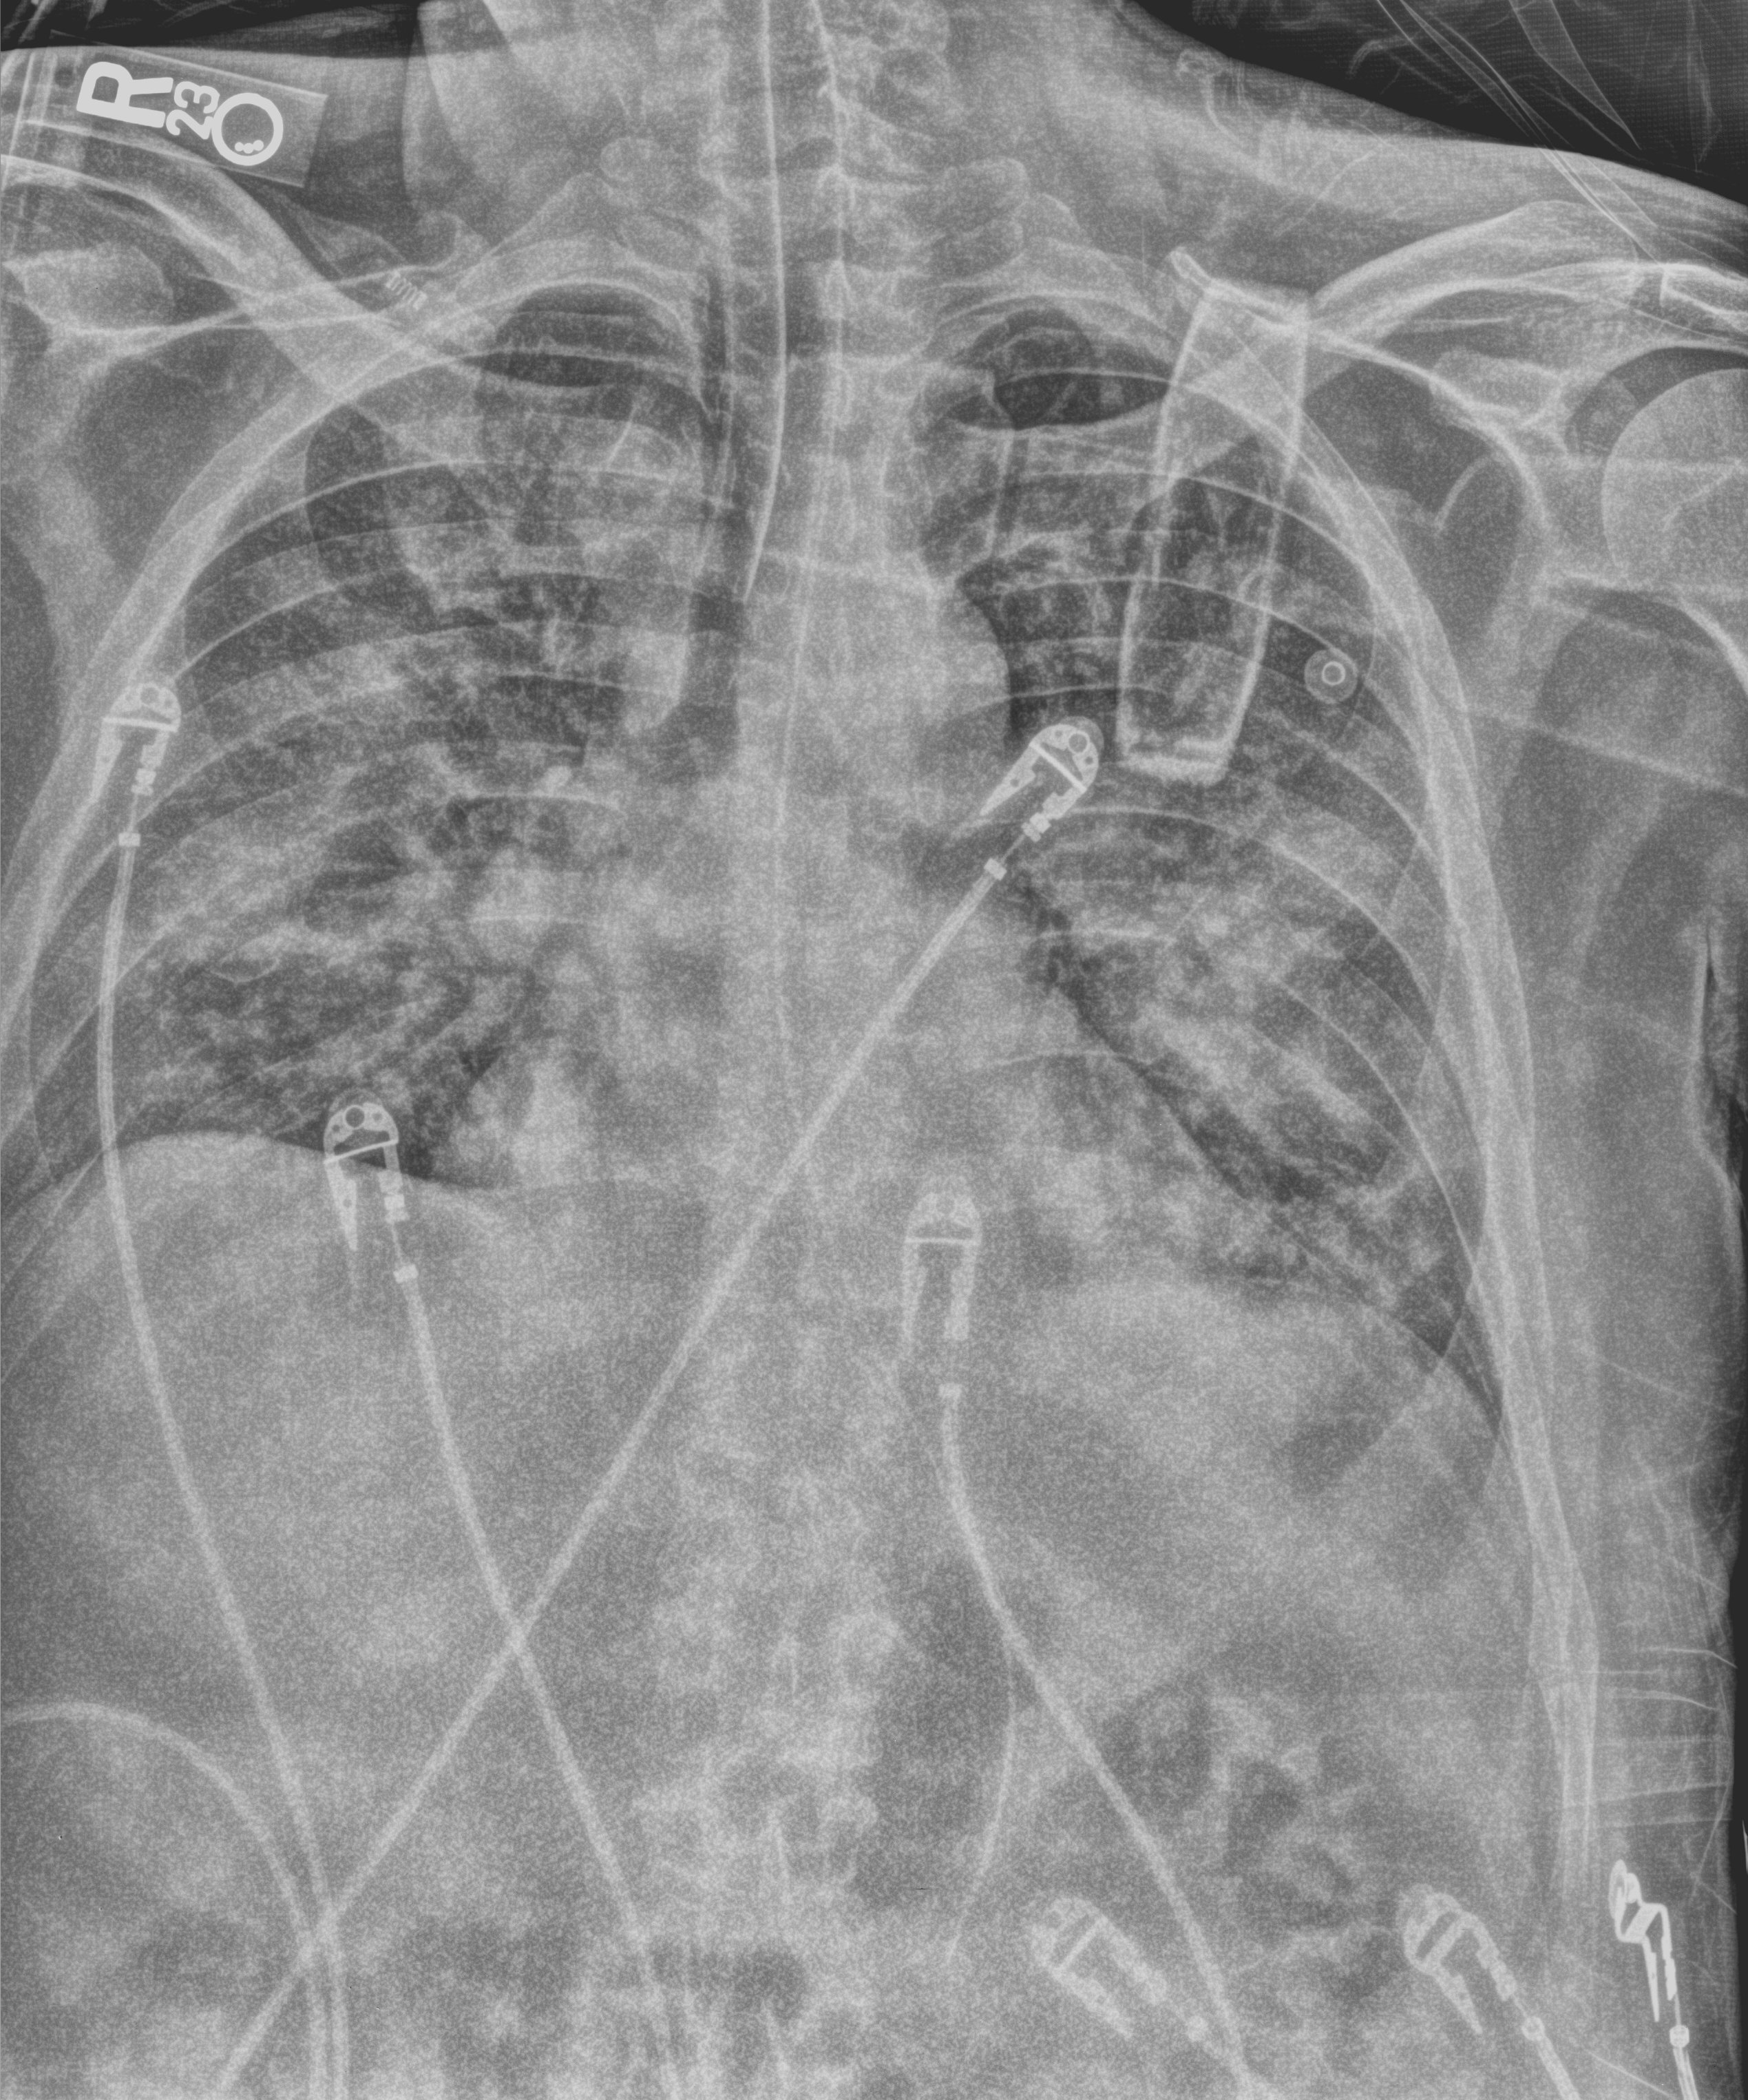
Chest X-ray (portable), anteroposterior (AP) projection. Male patient hospitalised with COVID-19, age 18–59 years.
Hospital-stay facts (about this admission, not read from this image; timing relative to this image not recorded):
- admitted to intensive care during this hospital stay: yes
- mechanically ventilated during this hospital stay: yes